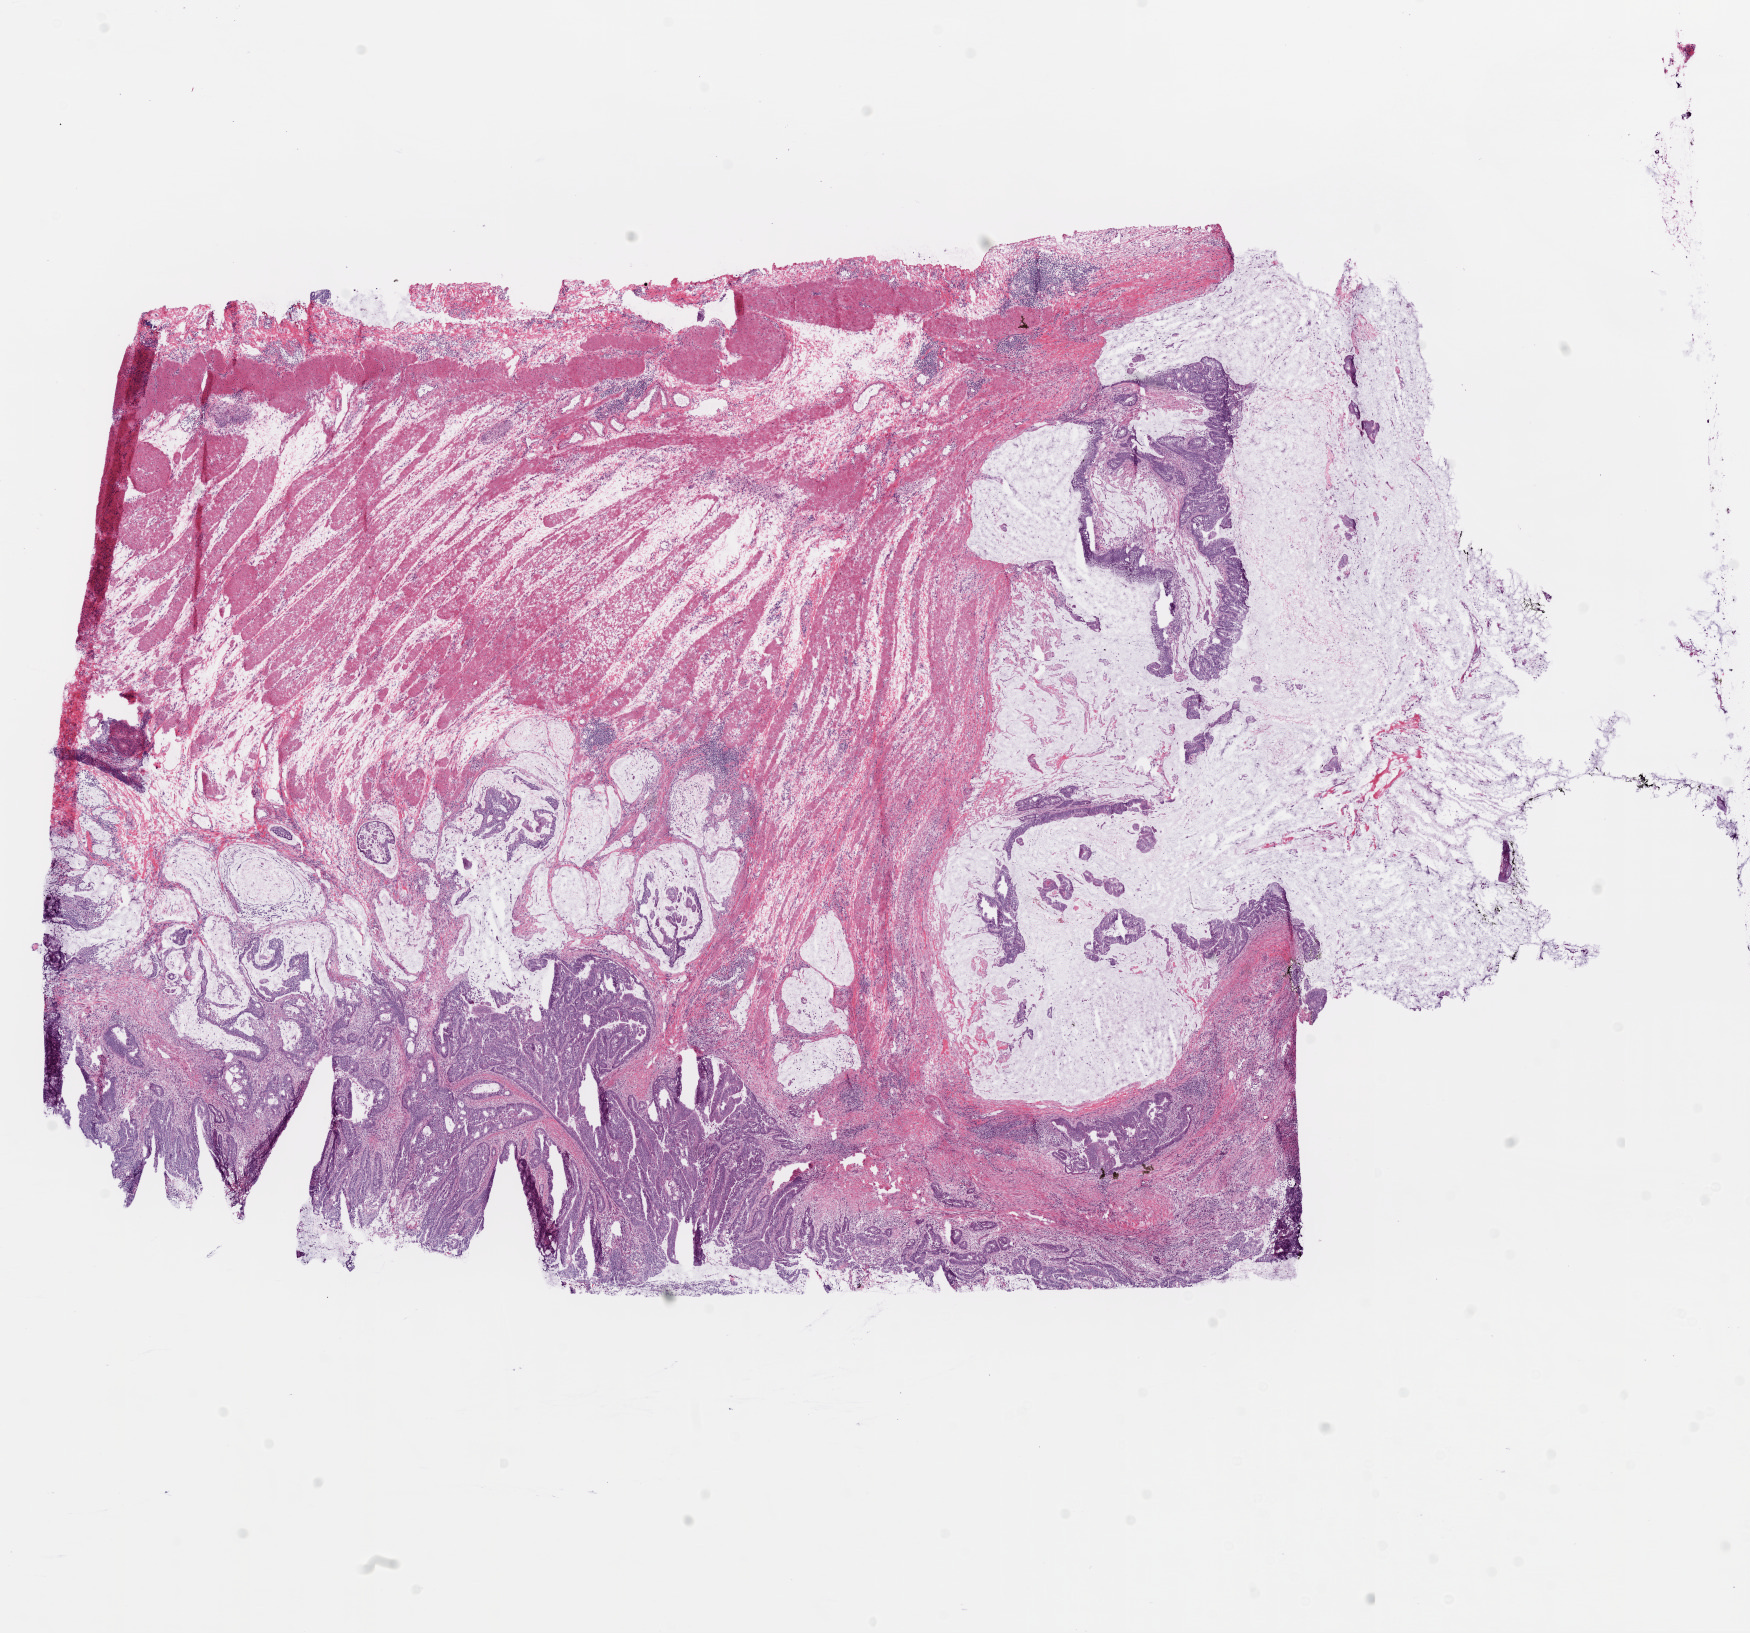
Hematoxylin and eosin (H&E) stained whole-slide image, shown as a low-resolution overview of the whole scanned area (about 14.0 x 13.1 mm, slide scanned at 20x). Frozen section from the bottom of the tissue portion. Primary tumour sample from the colon. Patient: male, age at initial diagnosis 73 years. Slide review estimates, as recorded: tumour nuclei 65%, normal cells 30%, stromal cells 5%, necrosis 0%.
• TNM: T3 N0 M0
• diagnosis: Adenocarcinoma, NOS
• lymph nodes positive (case pathology): 0 of 24 examined
• AJCC pathologic stage: IIA